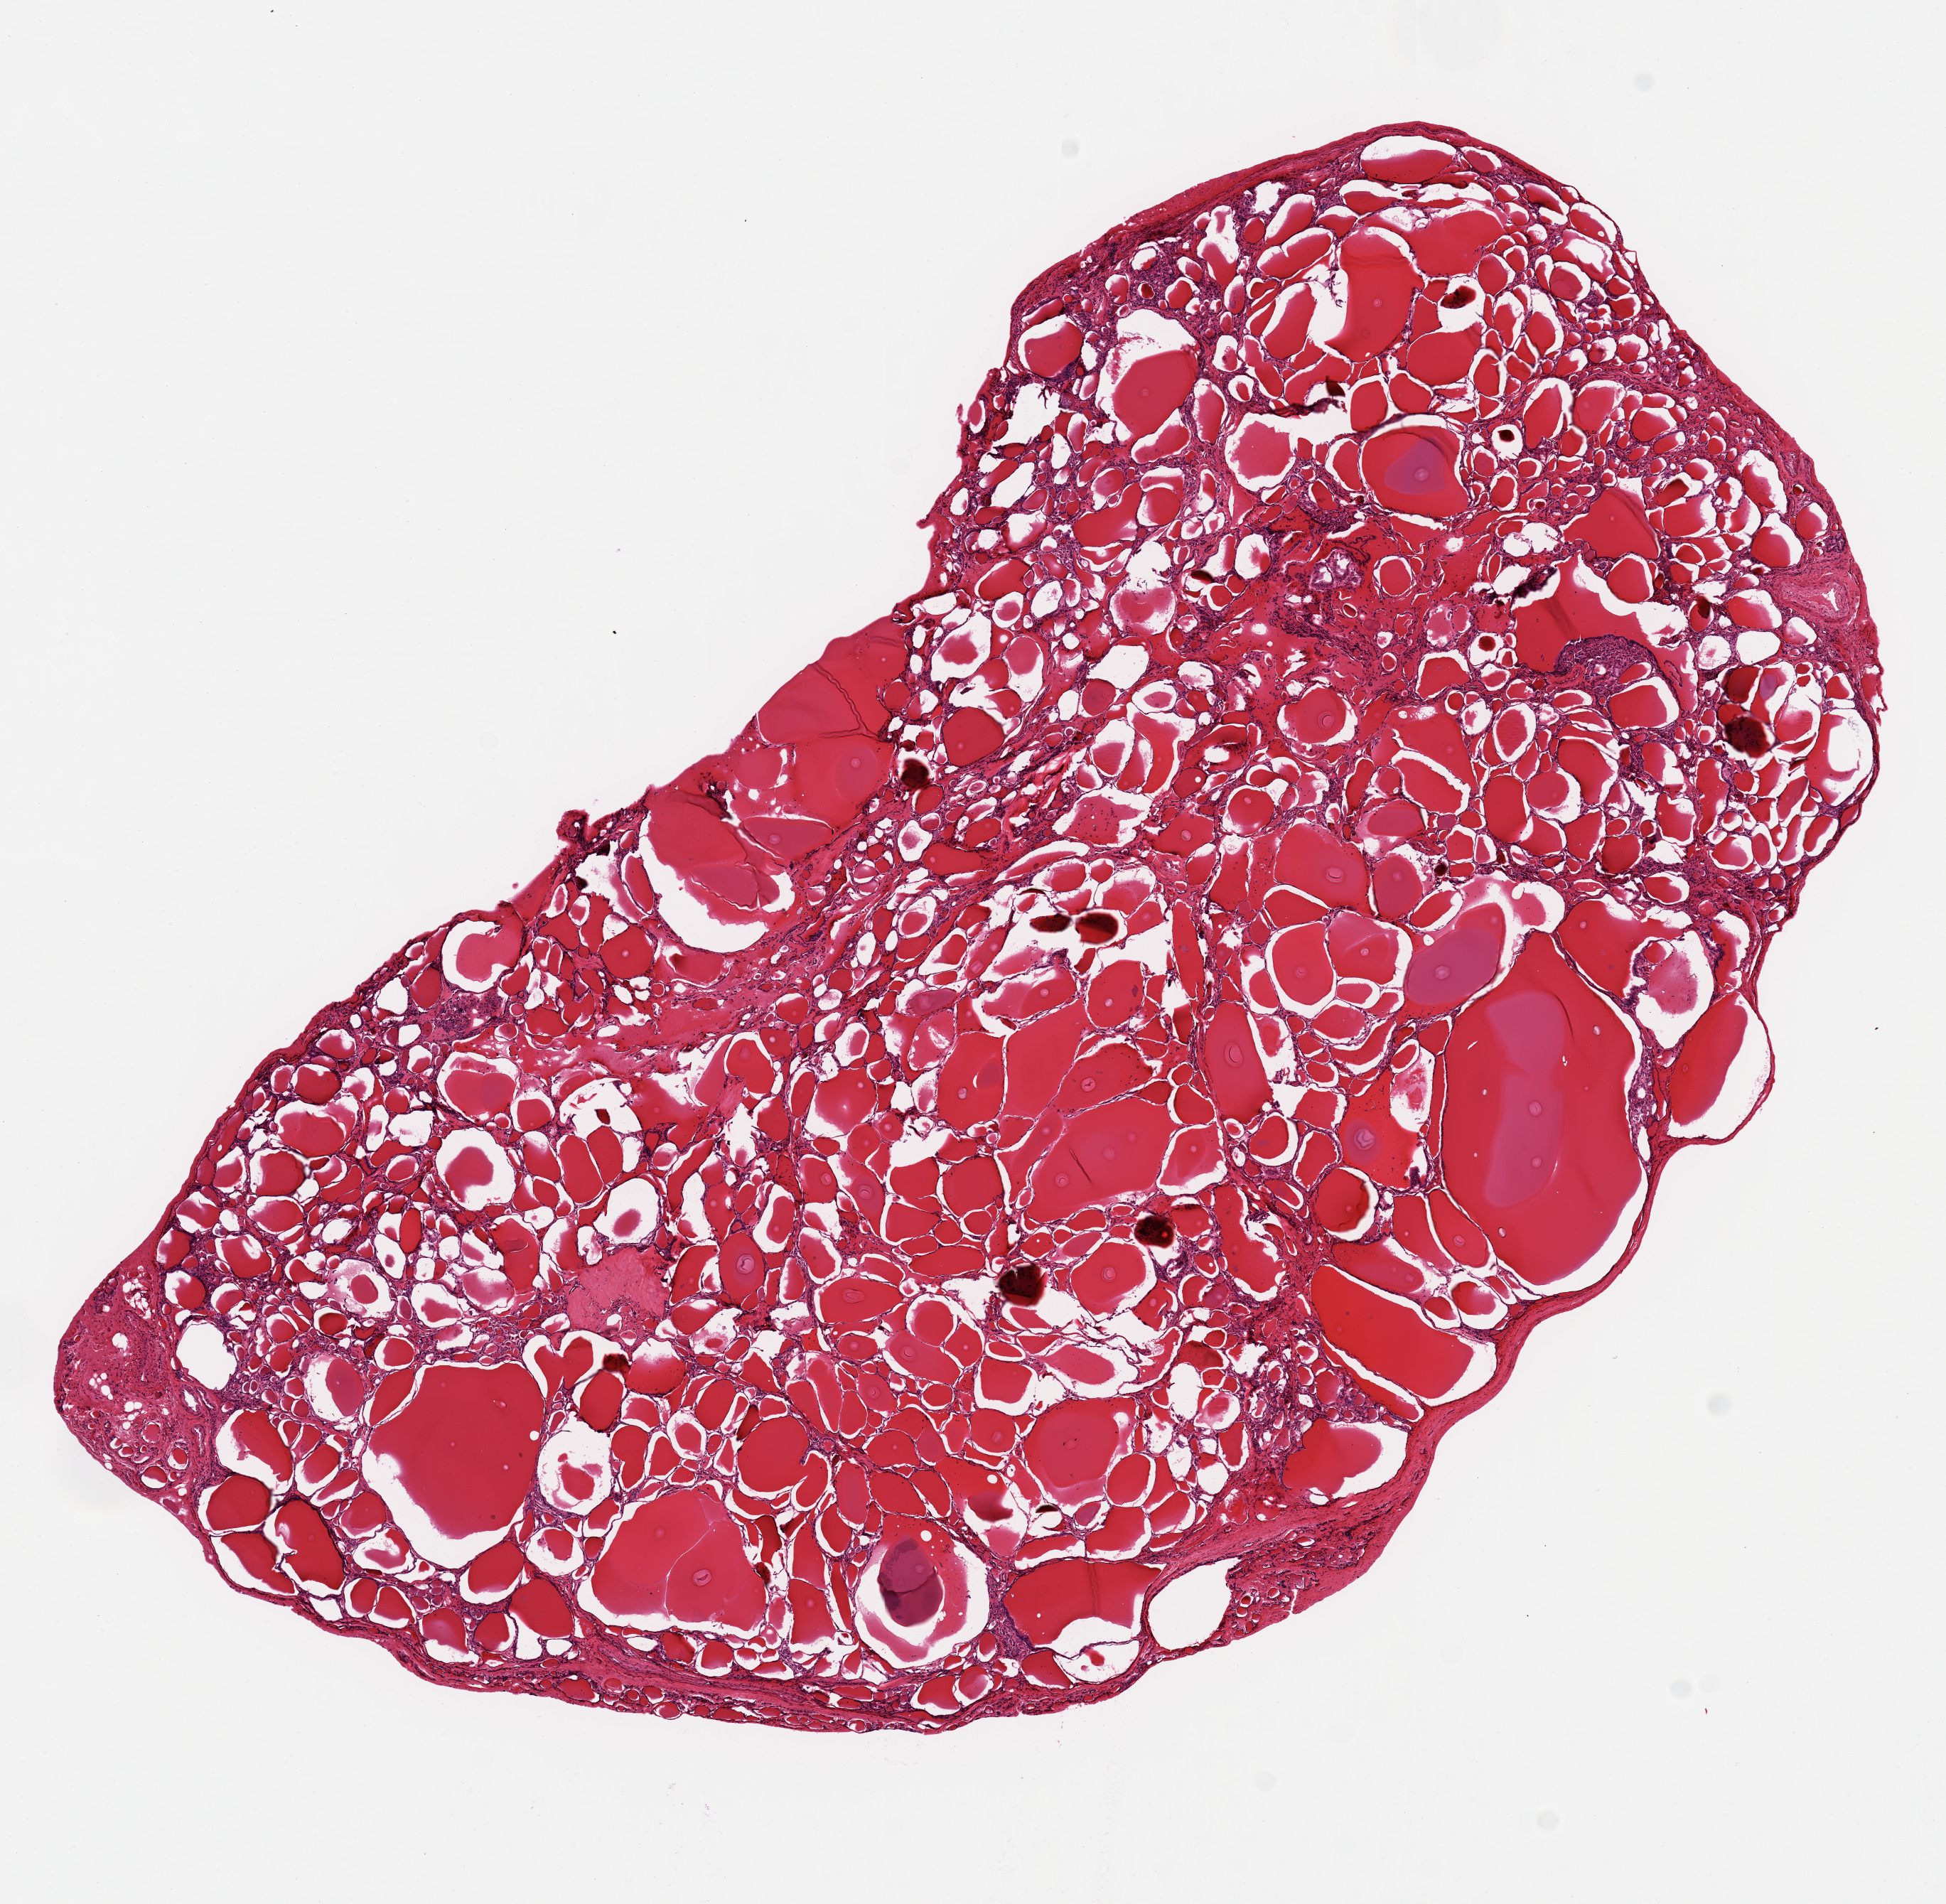
Digitized haematoxylin and eosin-stained section — whole scanned area (about 10.8 x 10.6 mm) shown as a low-resolution overview; PAXgene-fixed paraffin-embedded (PFPE) section; section of thyroid (target tissue); tissue donor sample. Male donor.
* reviewer comment on this tissue sample: 10x6 mm